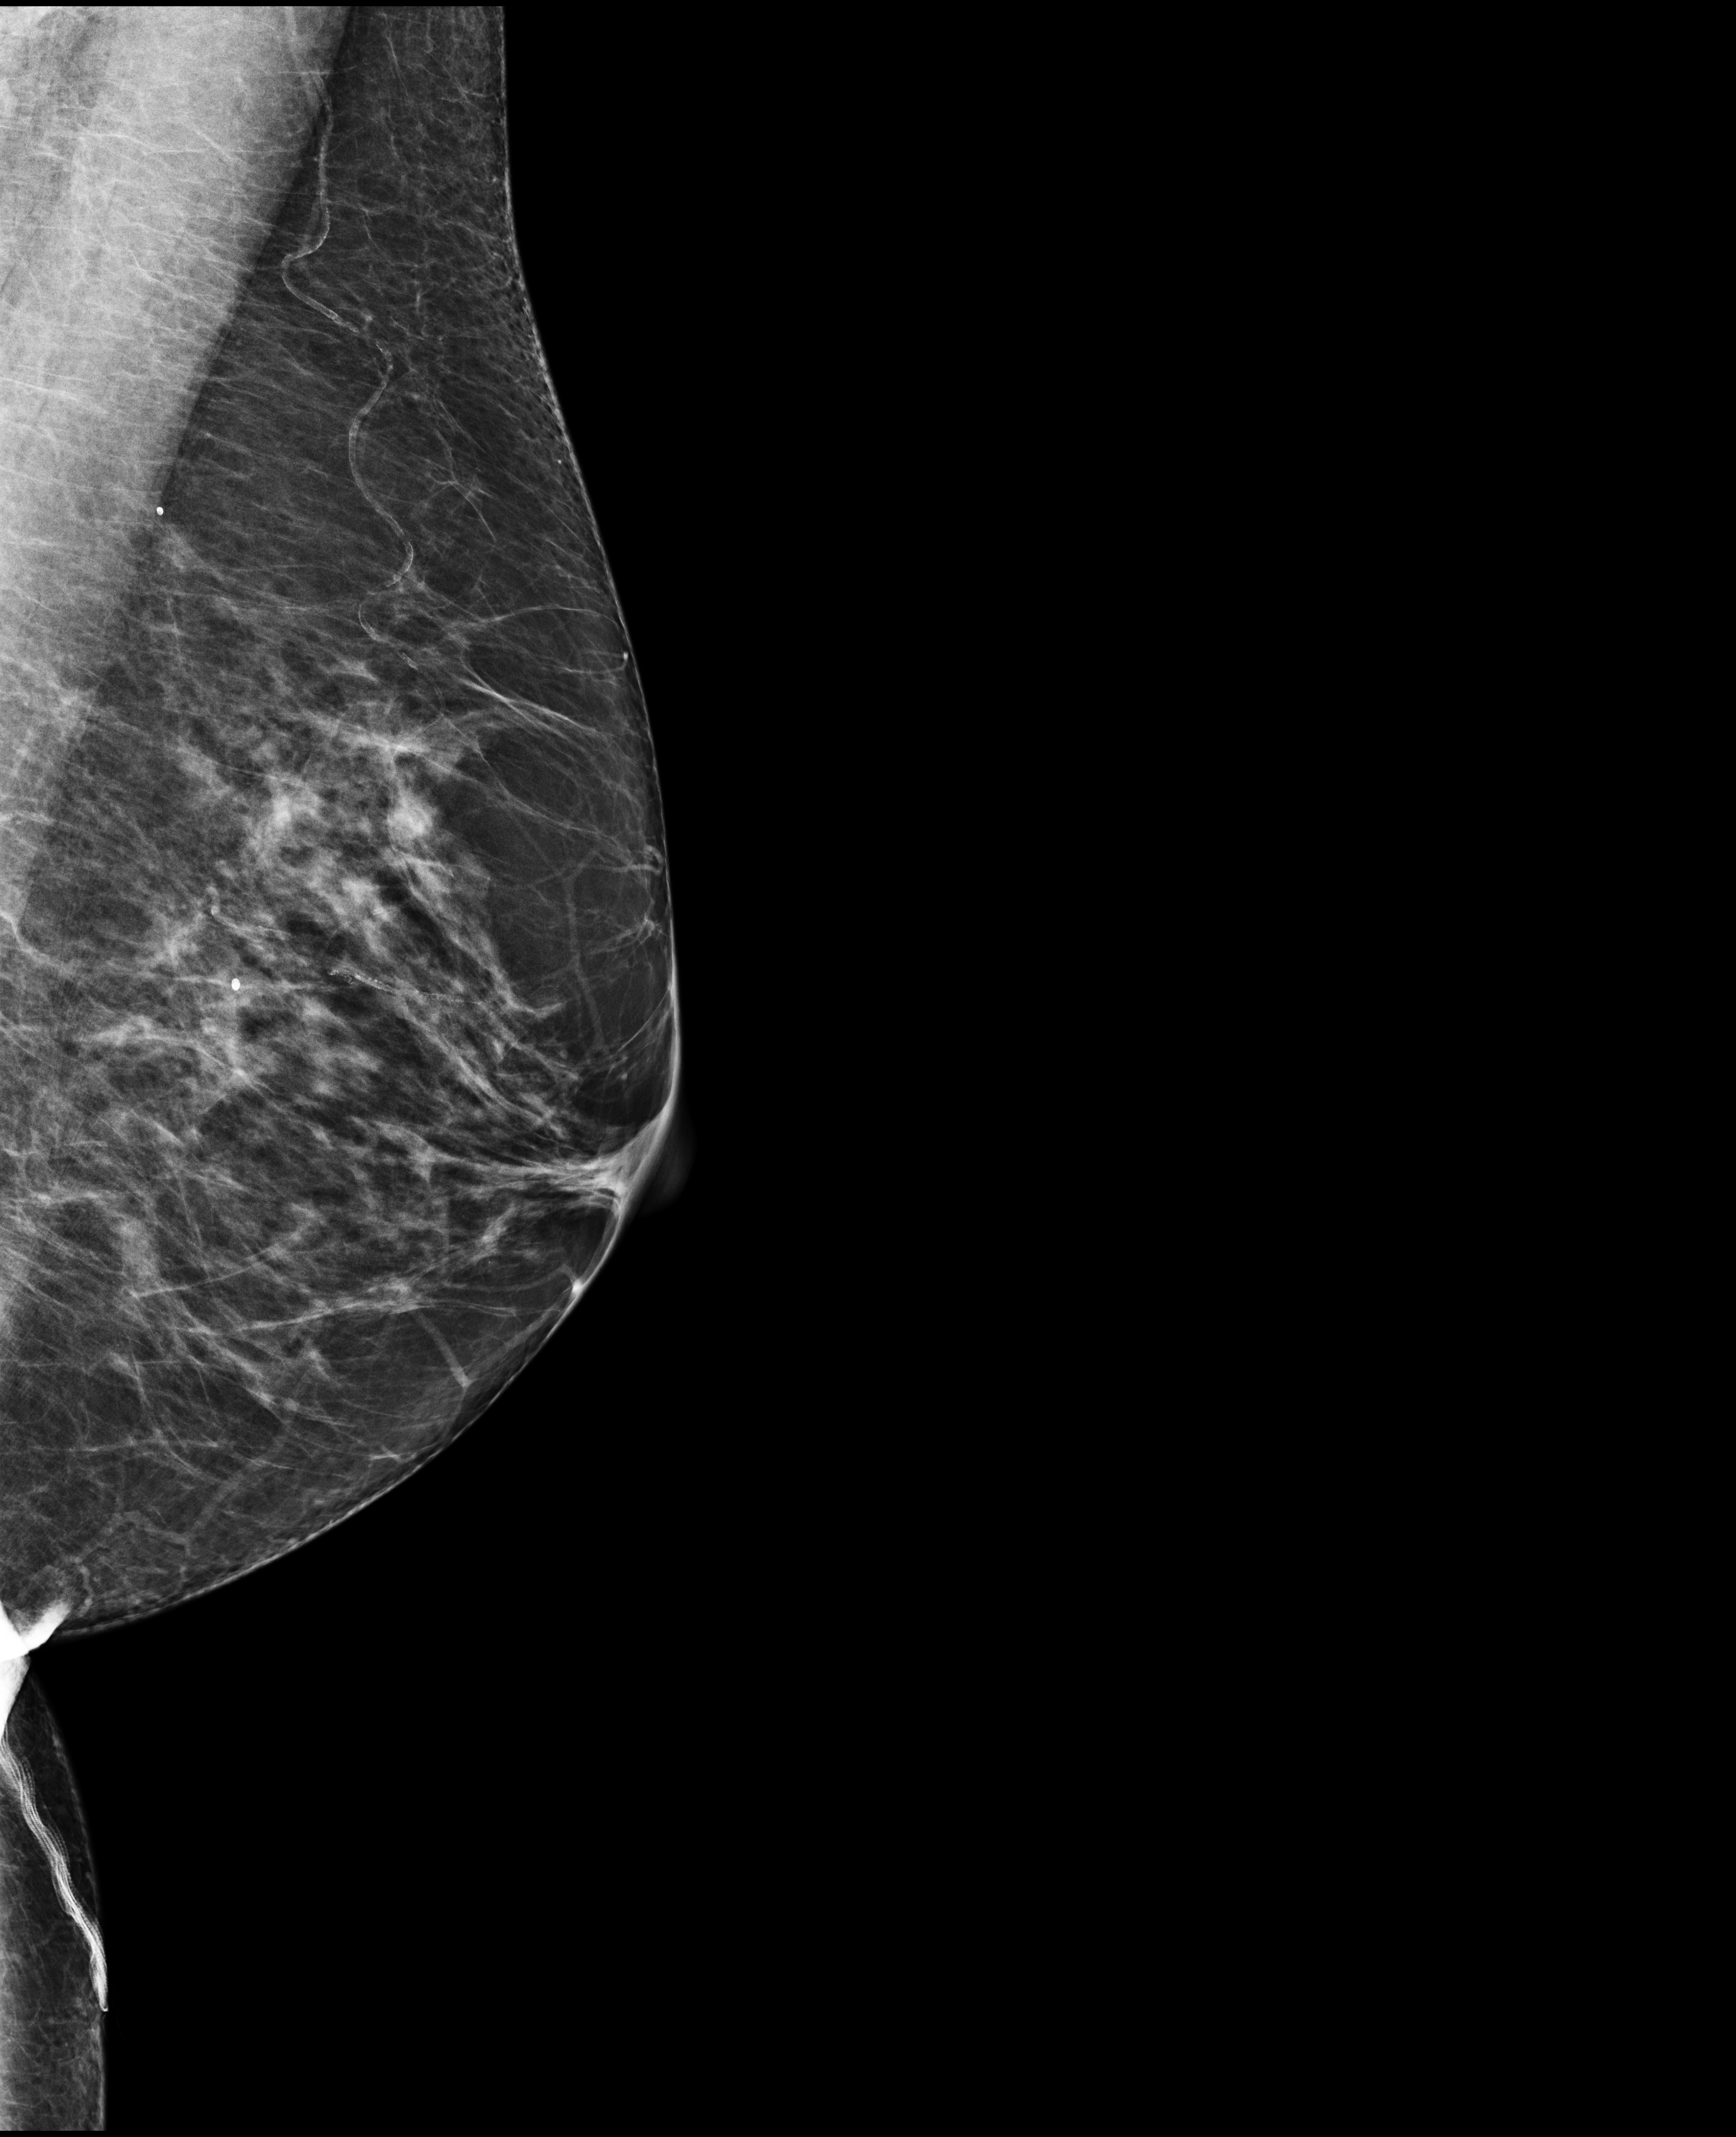
Screening examination. Patient aged 68 years (female).
Image type: full-field digital mammogram. Breast: left. Projection: medio-lateral oblique projection.